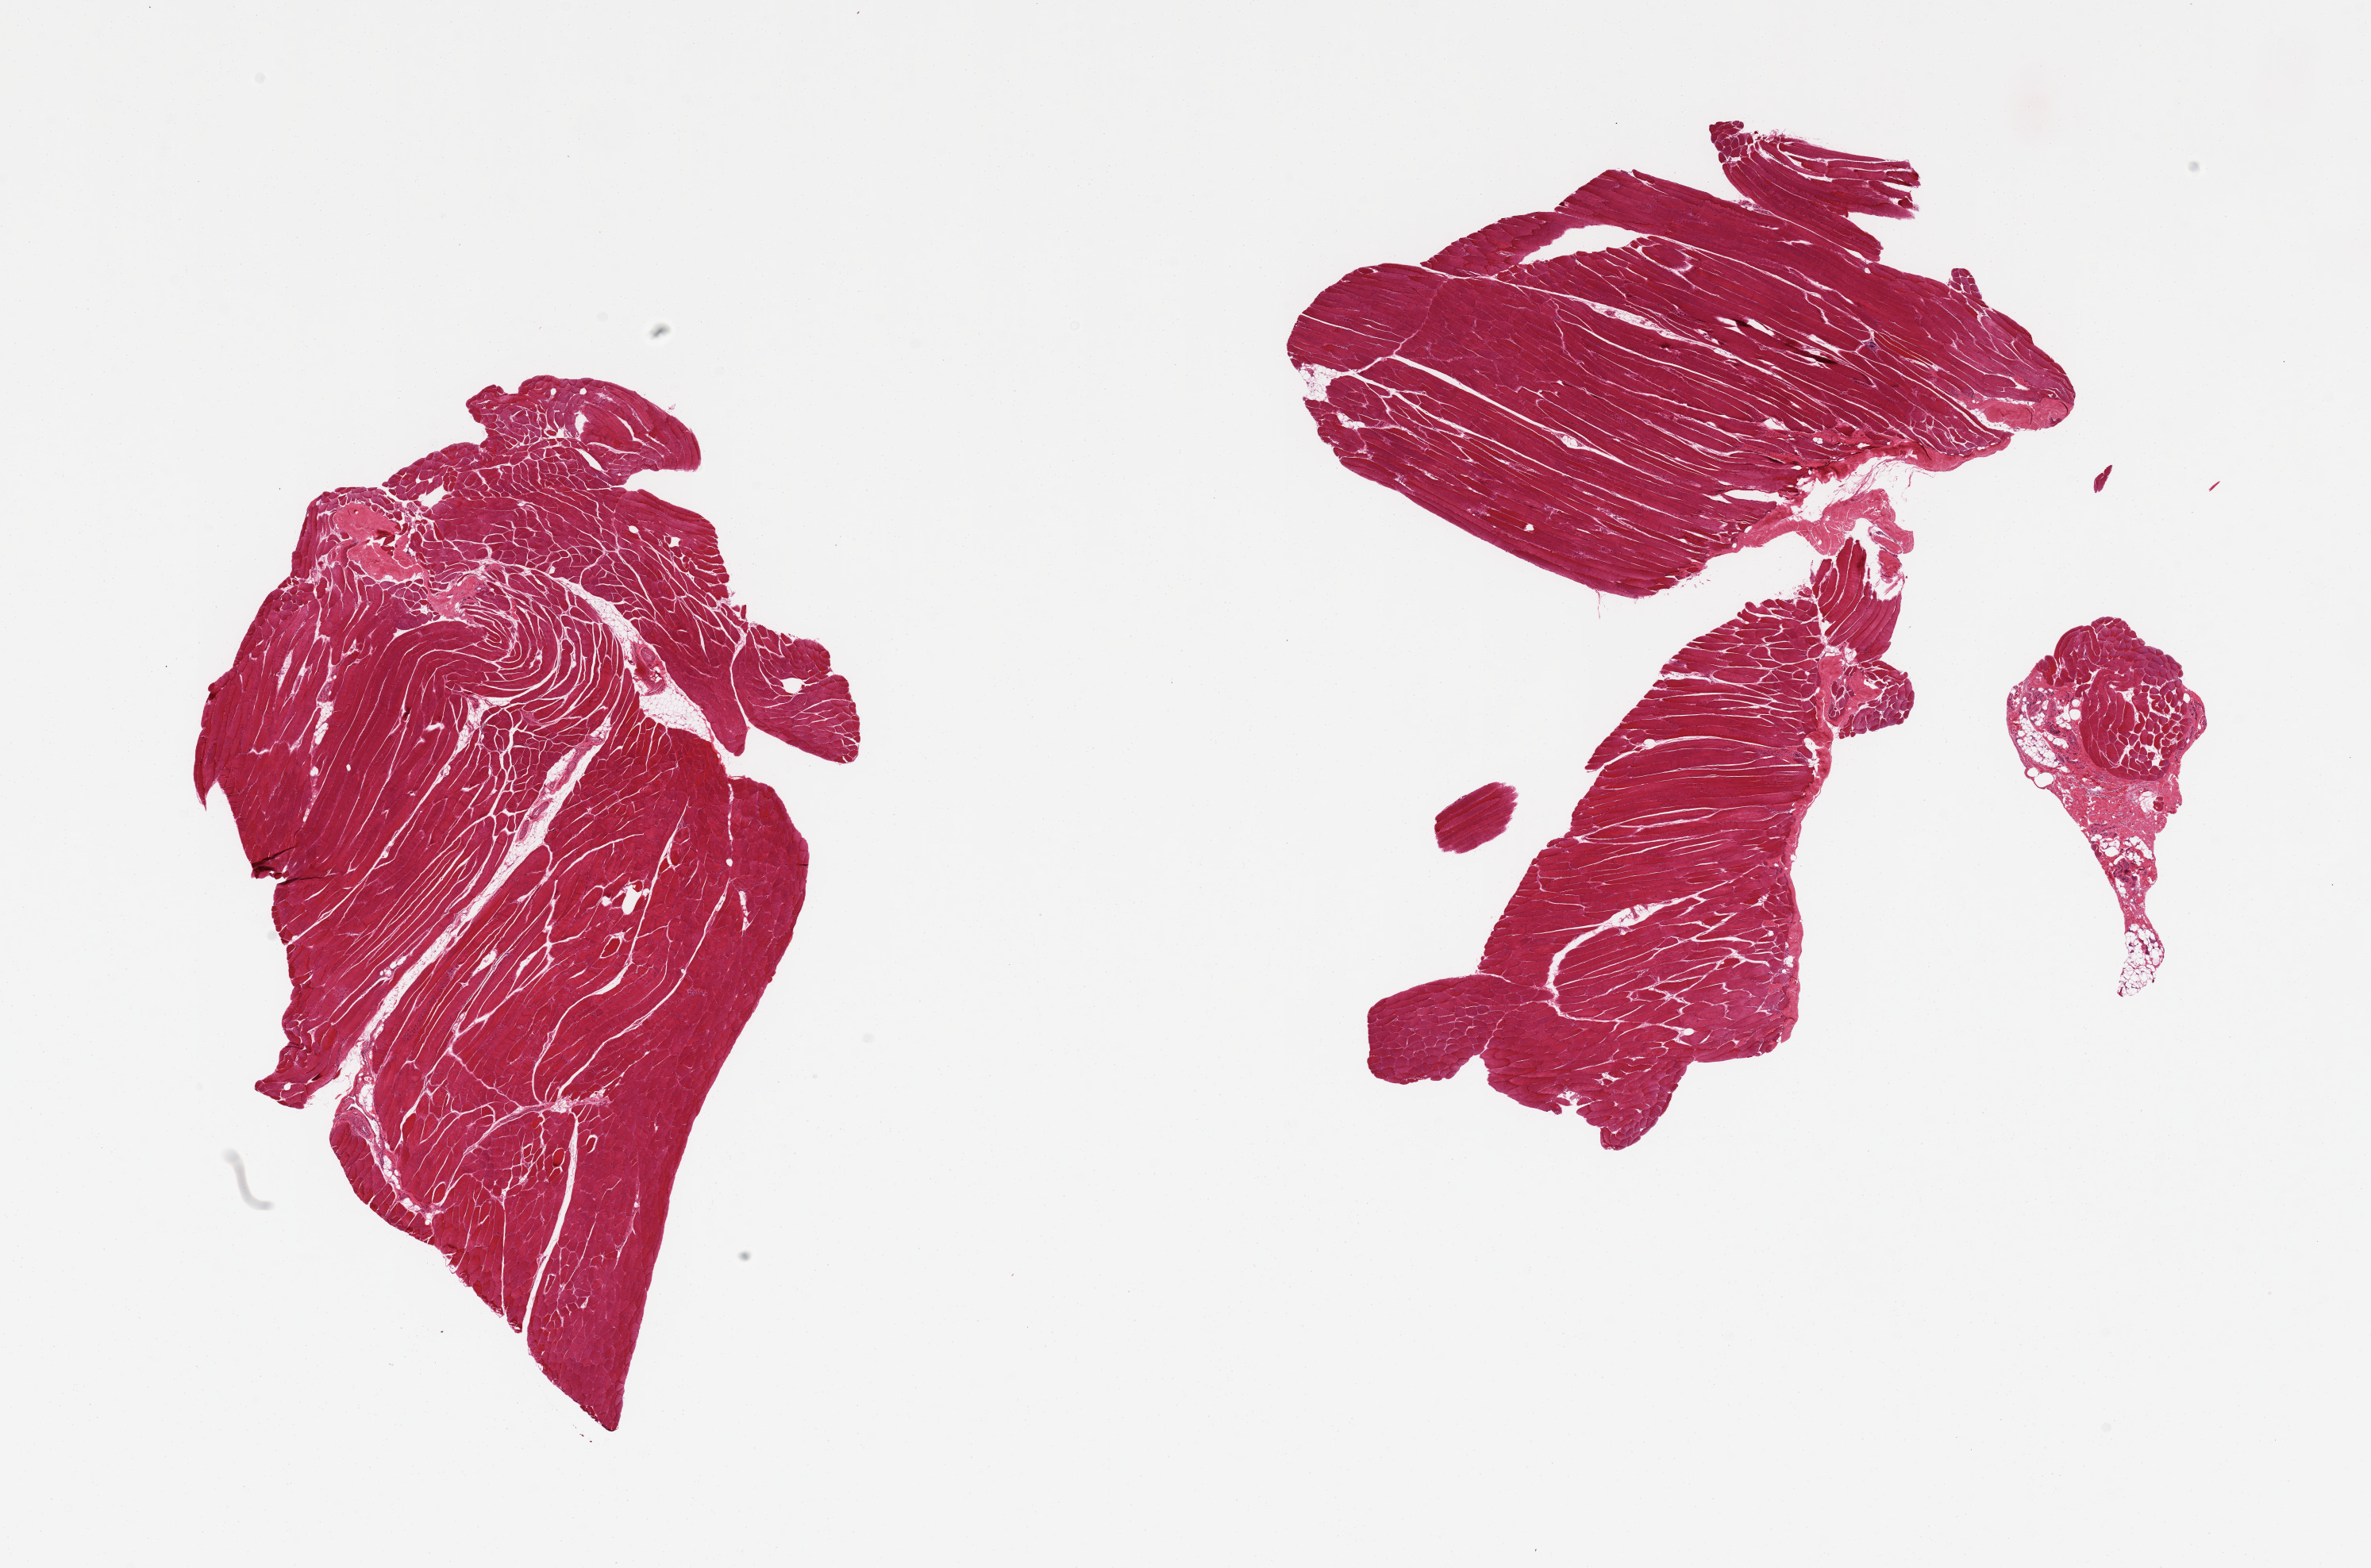
H&E whole-slide image, brightfield, a low-resolution overview of the entire scanned area, about 23.6 x 15.6 mm; PAXgene-fixed paraffin-embedded (PFPE) section; section of skeletal muscle (target tissue); tissue donor sample. Donor: male.
* reviewer comment on this tissue sample: 2 pieces, skeletal muscle with only scant adipose tissue, small portion of tendon and fibrovascular tissue